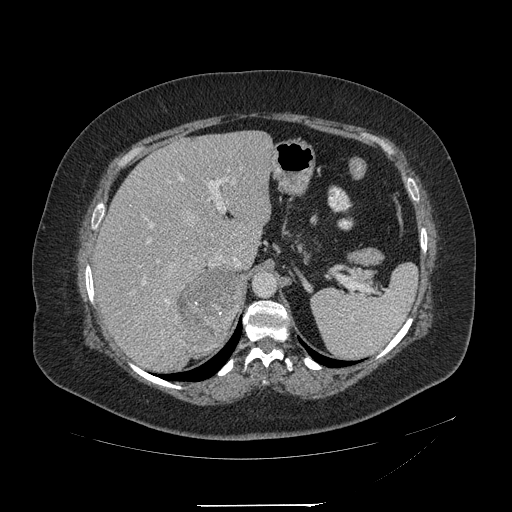
Contrast-enhanced abdominal CT, one axial slice. Slice 150 of 217 in the series (ordered by position). Reconstruction kernel STANDARD. 120 kVp. Intravenous contrast given. Soft-tissue window (W 400 / L 40 HU). 1.25 mm slice thickness. 512 × 512 image matrix. Patient: female, 55 years. From the clinical record (not read from this slice): diagnosis: adrenocortical carcinoma; tumour side: right adrenal; tumour size at pathology: 11 cm; Ki-67 index: 20 %; stage (as recorded): 2.
Annotated regions visible in this slice (semi-automatically segmented with operator editing):
- mass: bounding box [x1, y1, x2, y2] px = [179, 268, 241, 351]